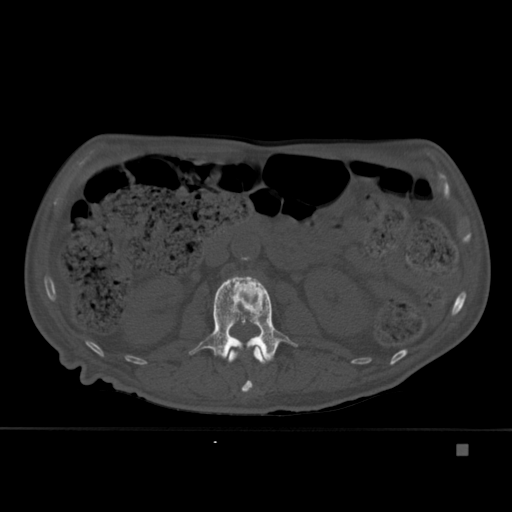
CT including the spine, one axial slice; position 165 of 451 along the scan axis; bone window (W 1800 / L 400 HU); 1.5 mm slice thickness; 512 × 512 image matrix, field of view 378 × 378 mm. Male patient, age 75 years. From the clinical record (not read from this slice): primary cancer: prostate.
Structures marked on this image (semi-automatically segmented with operator editing):
- L1 vertebra: bounding box [x1, y1, x2, y2] px = [227, 347, 268, 392]
- L2 vertebra: [188, 276, 298, 361]